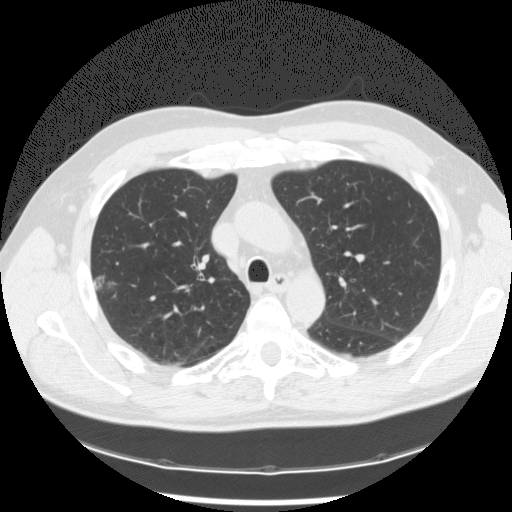
Axial slice from a low-dose chest CT screening exam, baseline screening round, lung window (W 1500 / L -600 HU), 2.5 mm slice thickness, slice 40 of 119 in the series, 512 × 512 image matrix, field of view 360 × 360 mm. Male participant, aged 62 years at enrolment. Former smoker at enrolment.
• Expert reader's lesion annotation, bounding box (x1, y1, x2, y2) in pixels: (88, 268, 122, 301).
• Reader record for this screening exam (exam-level; its link to the box is not recorded): non-calcified nodule or mass ≥4 mm, right upper lobe, 14 × 11 mm, poorly defined margins, mixed attenuation.
• Lung cancer was diagnosed 343 days after this screen: adenocarcinoma, NOS, right upper lobe, poorly differentiated (G3), stage IIB (AJCC 6th edition), 5 mm at pathology.